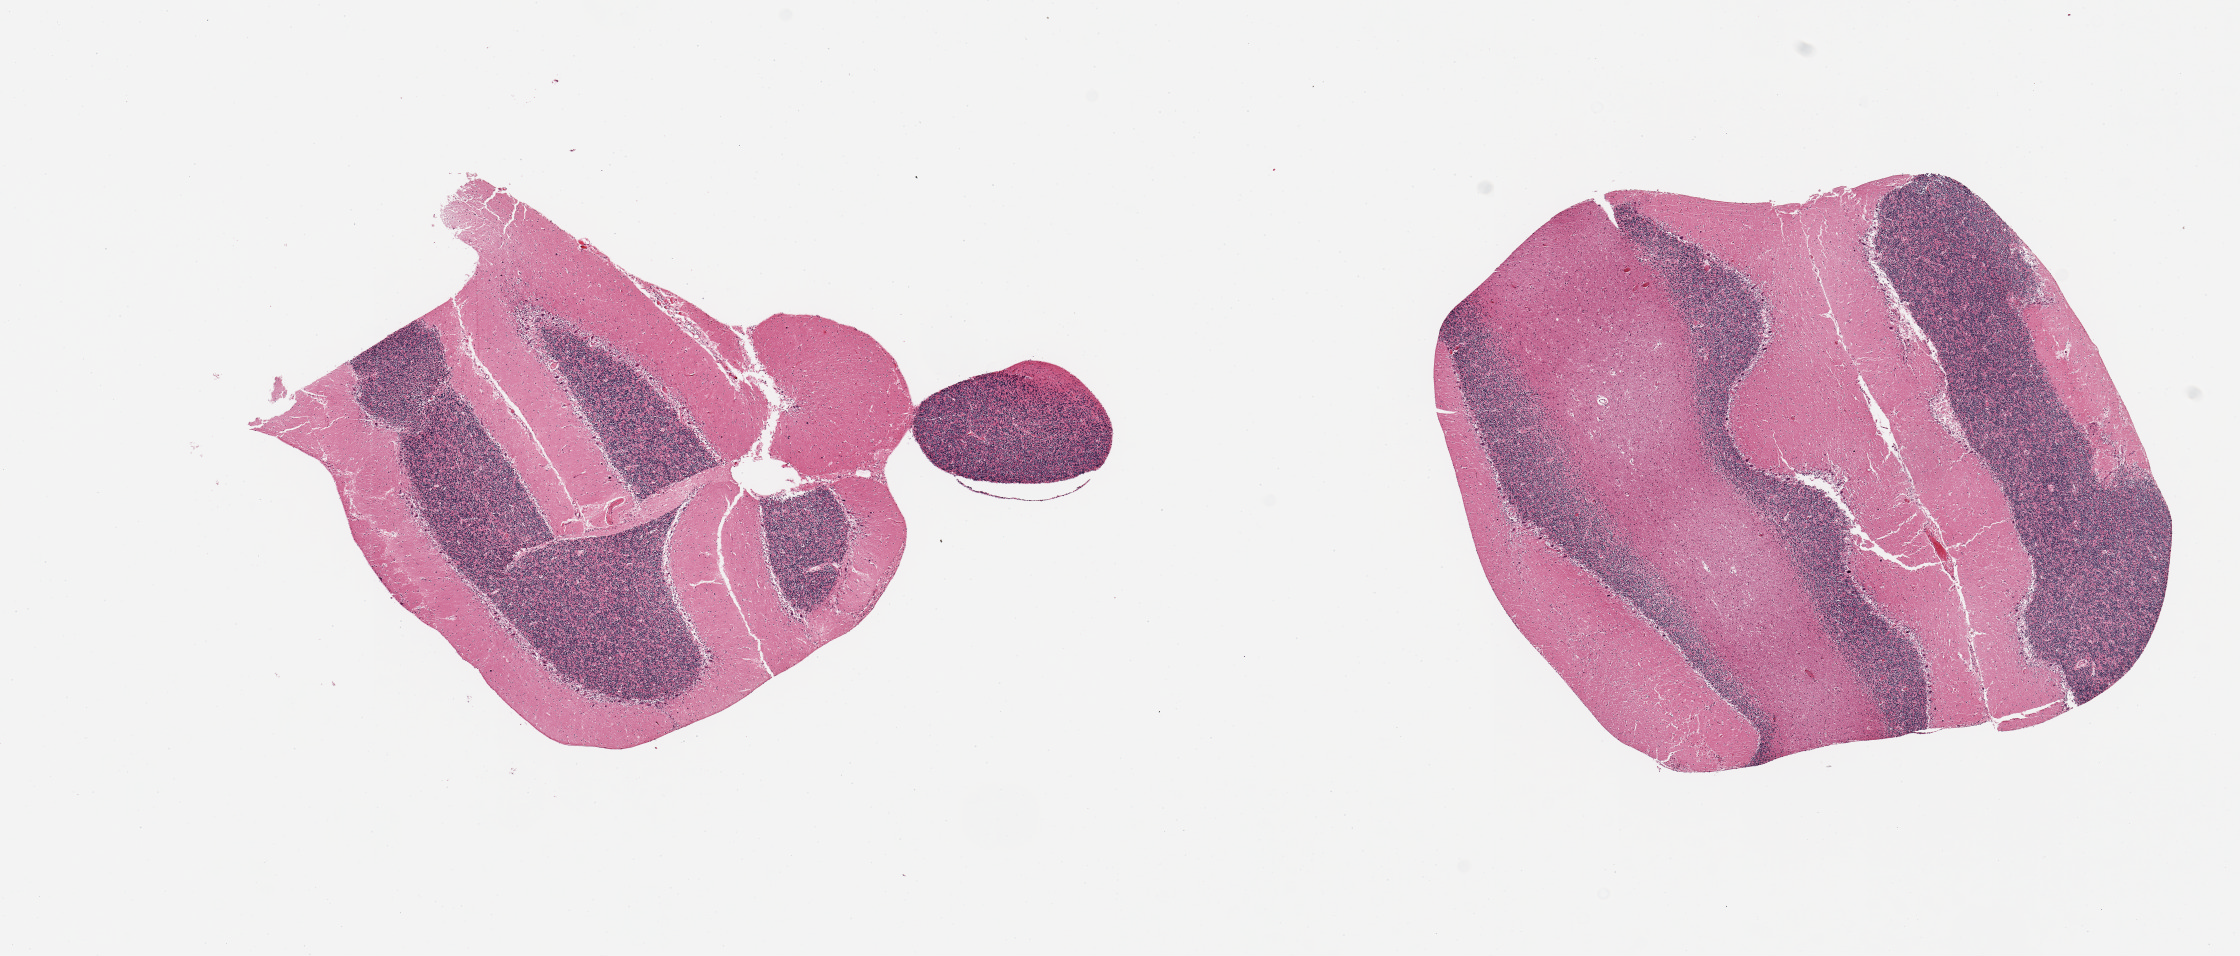
Whole-slide image, hematoxylin and eosin (H&E) stain, brightfield — low-resolution overview of the scanned area, about 17.7 x 7.6 mm (from a 20x scan); PAXgene-fixed paraffin-embedded (PFPE) section; section of cerebellum (target tissue); donor tissue sample. Male donor.
Reviewer comment on this tissue sample: 2 pieces.